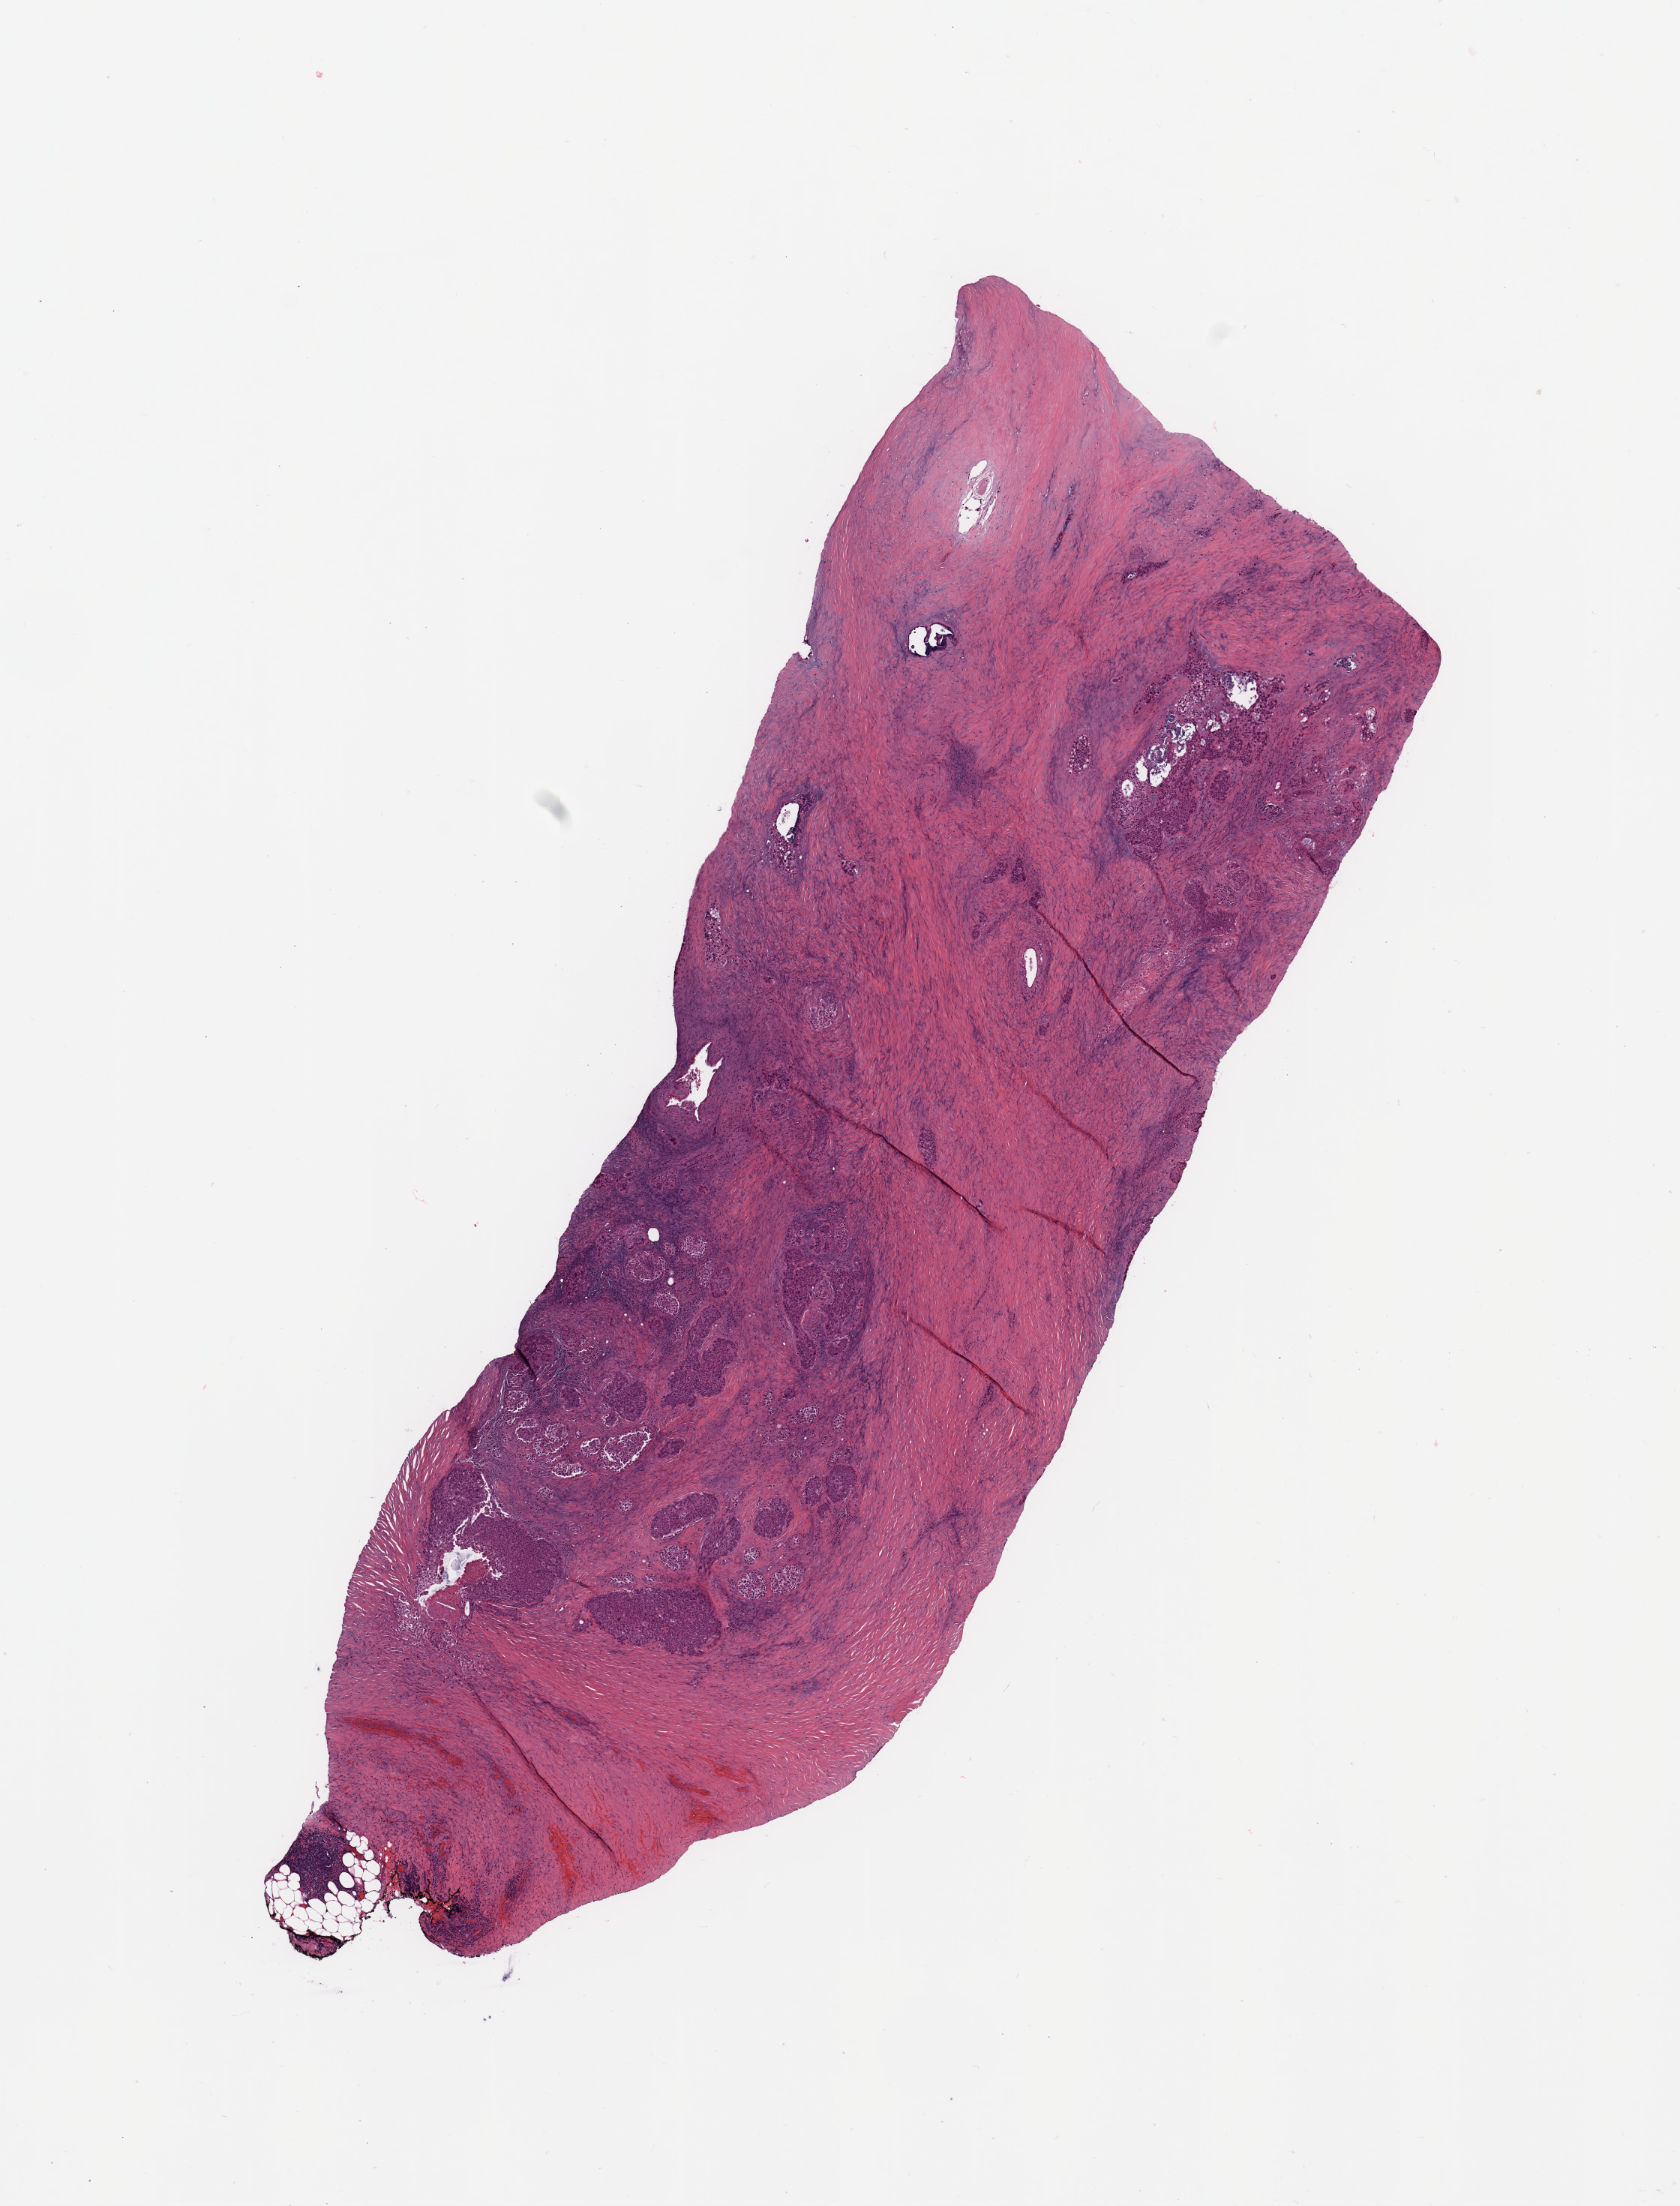
Digitized Hematoxylin and eosin (H&E) stained tissue section (whole slide) — whole scanned area (about 8.9 x 11.6 mm) shown as a low-resolution overview. Tumour tissue sample, pancreas. Patient: male, age 69 years. Histologic grade: G2 (moderately differentiated).
Diagnosis: Infiltrating duct carcinoma, NOS. AJCC pathologic stage: IIA. Primary tumour site (as recorded): tail.